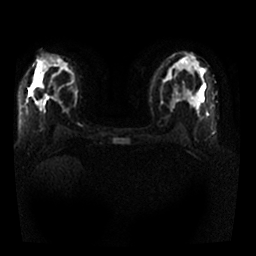
Breast MRI, one axial slice. Diffusion-weighted series; image 2 of 4 stored at this slice position (different b-values; order by instance number). 1.5 T. 4 mm slice thickness. 256 × 256 image matrix, field of view 330 × 330 mm. Female patient.
Structures marked on this image (outlined manually by an expert reader):
- tumour on diffusion-weighted imaging: box from (x=37, y=100) to (x=41, y=105) px